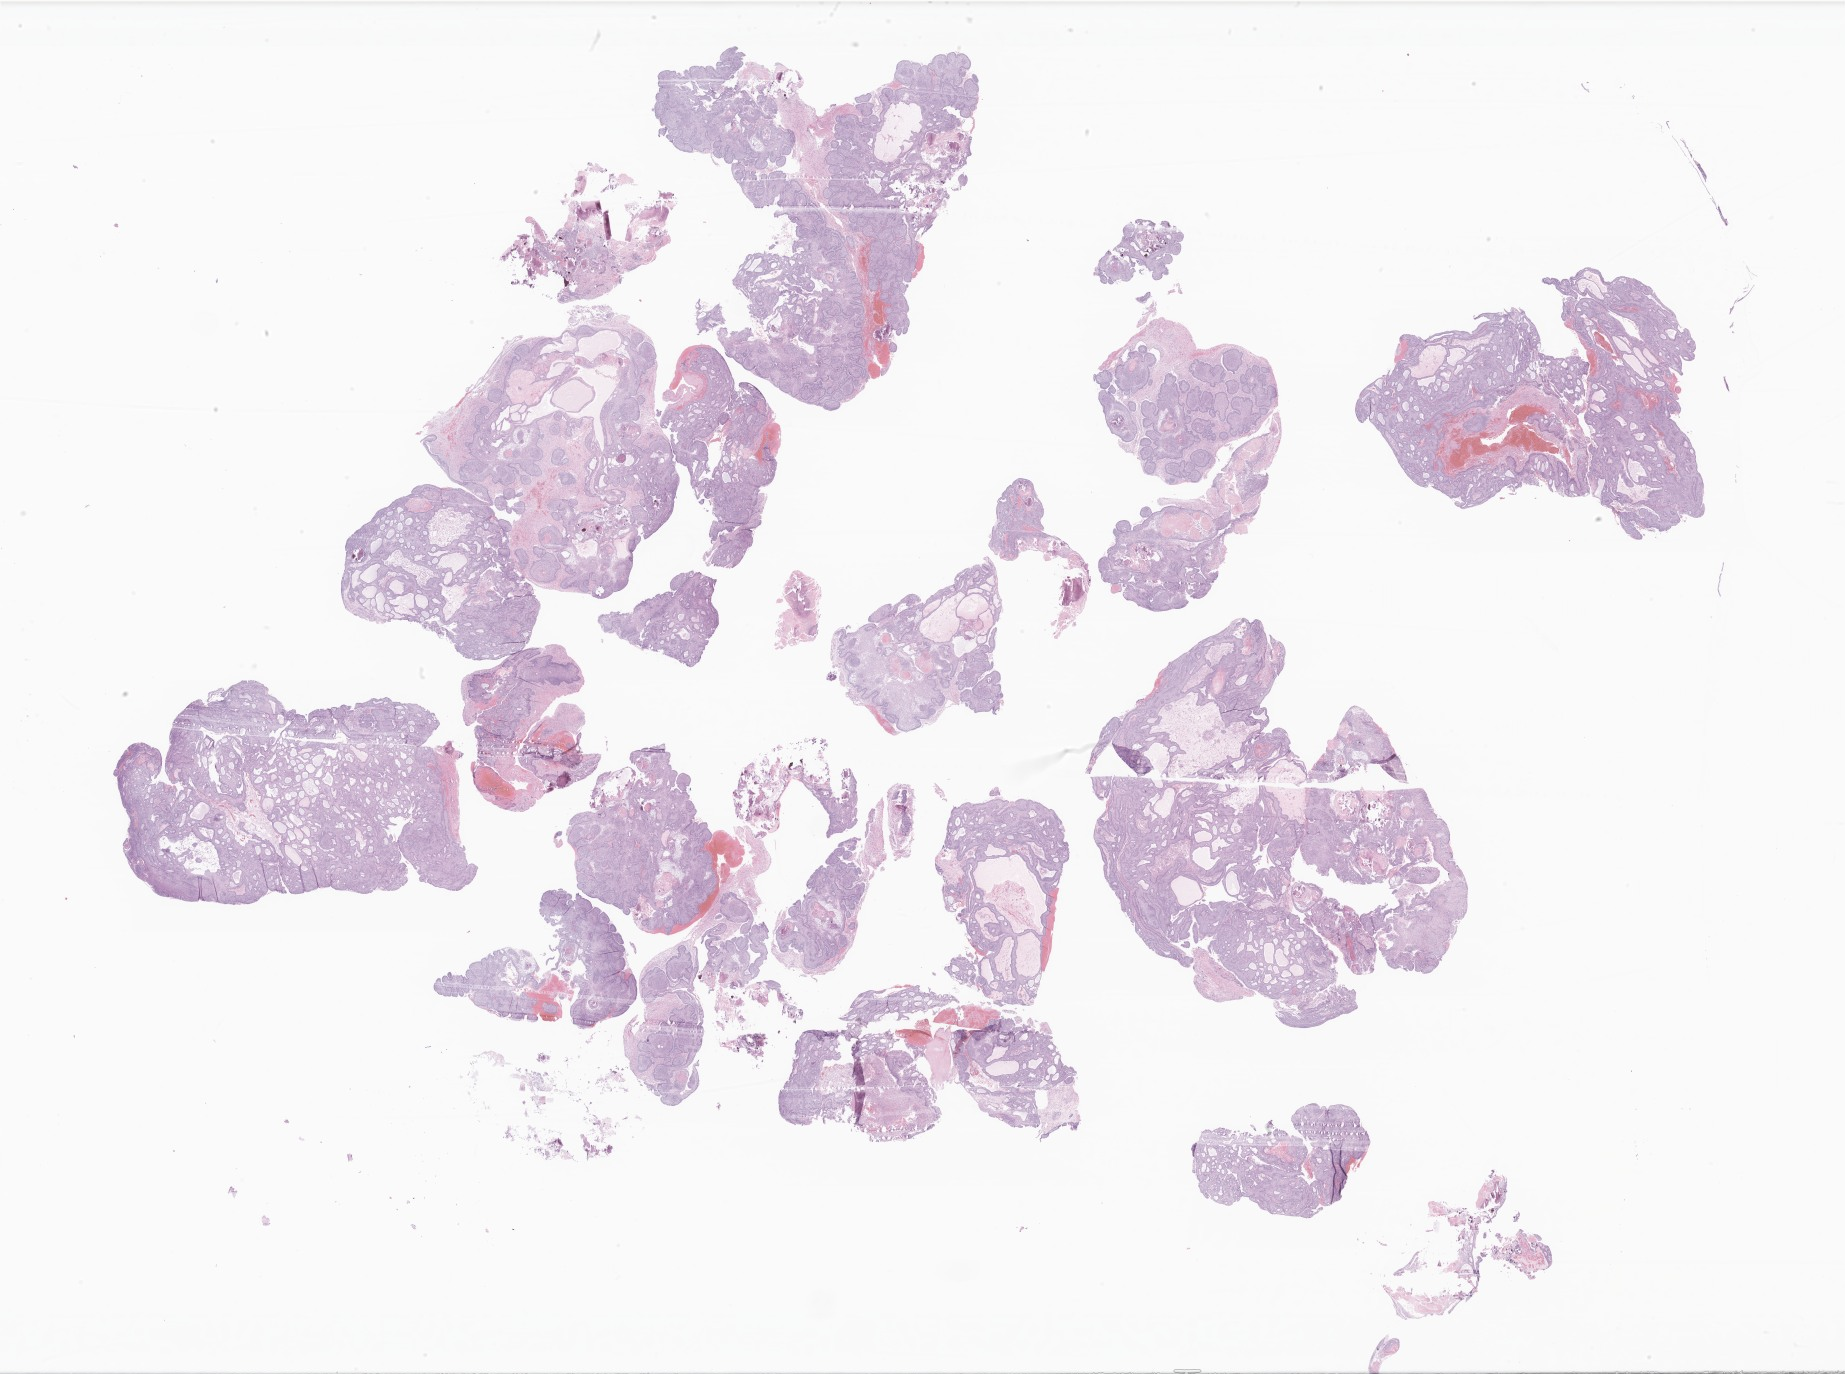
Digitized hematoxylin and eosin (H&E)-stained section of tumor tissue from the brain, a low-resolution overview of the entire scanned area, about 31.1 x 23.2 mm. FFPE section. Male patient, age 56 months.
Diagnosis (ICD-O-3 morphology term): Craniopharyngioma, adamantinomatous.